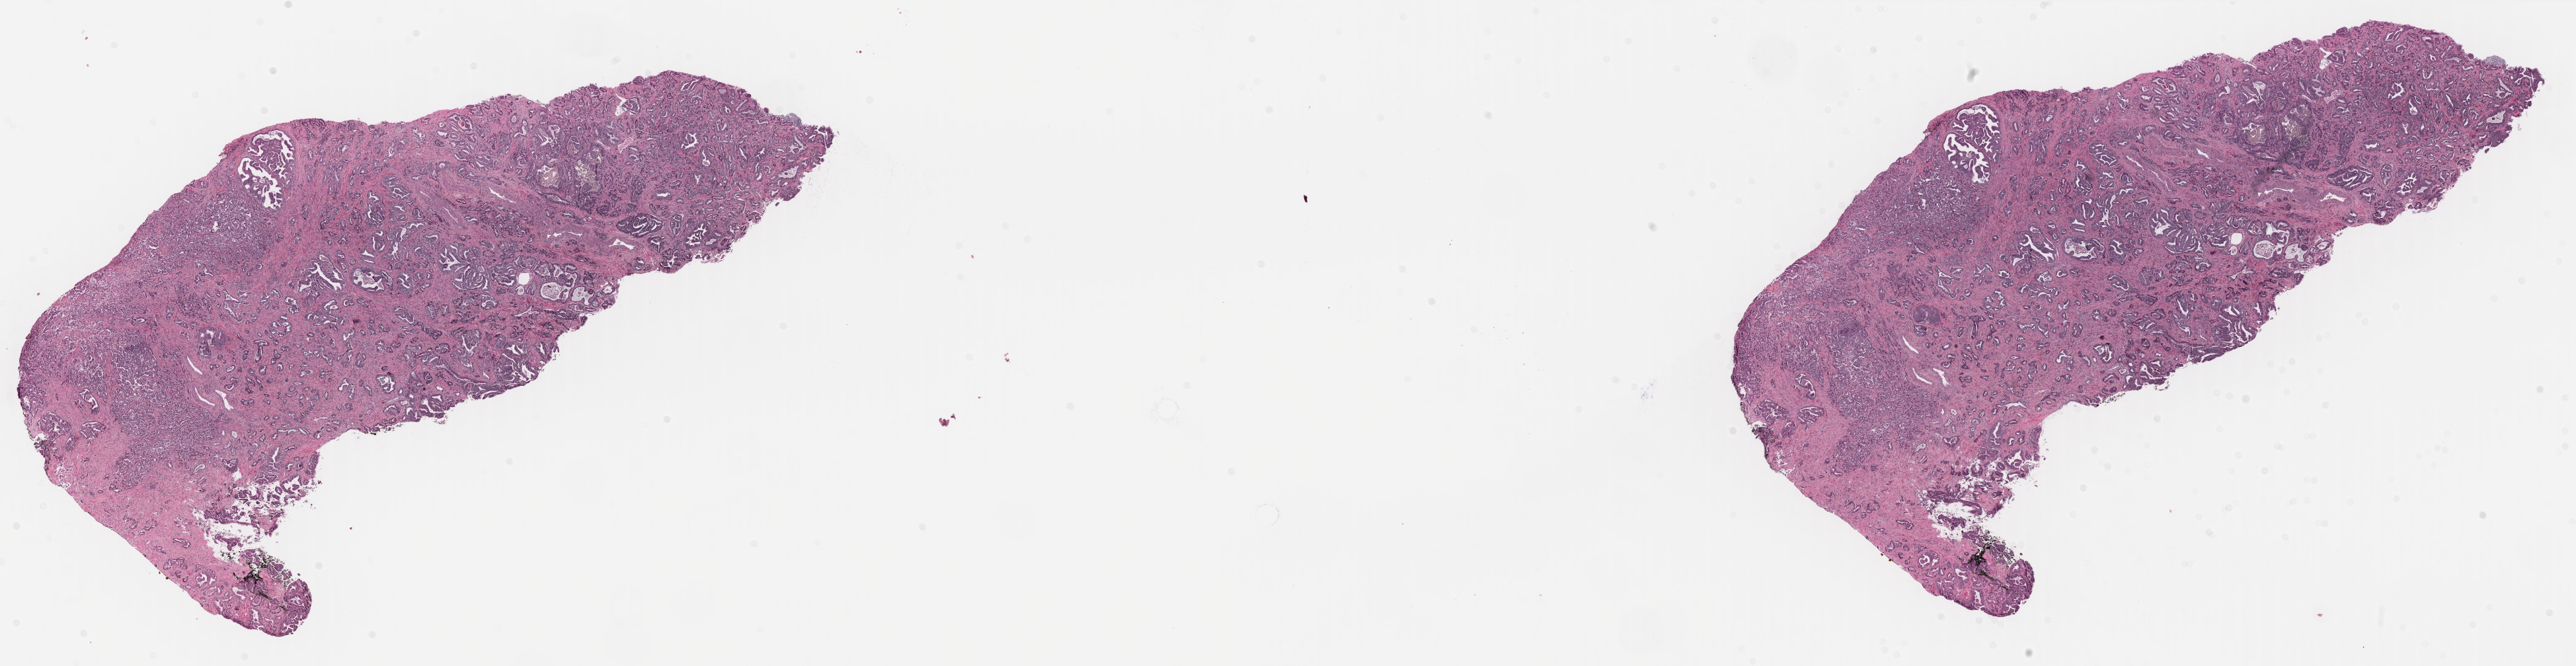
Hematoxylin and eosin (H&E) stained whole-slide image — whole scanned area (about 30.8 x 8.0 mm) shown as a low-resolution overview; formalin-fixed paraffin-embedded (FFPE) diagnostic section; prostate, primary tumour sample. Patient: male, age at initial diagnosis 56 years. Gleason score: 7 (4+3).
Histologic diagnosis: Adenocarcinoma, NOS (prostate gland). Lymph nodes positive (case pathology): 0 of 11 examined.